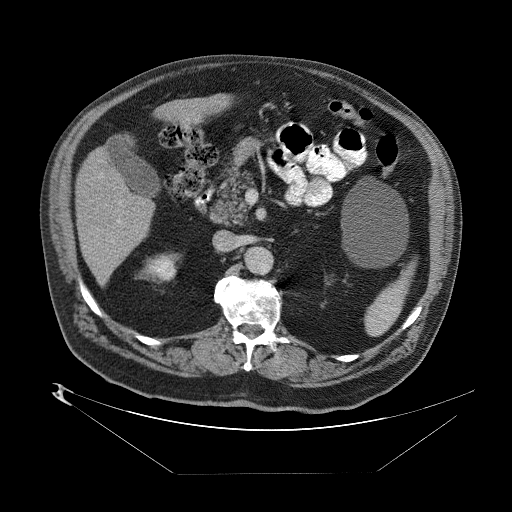
Contrast-enhanced abdominal CT (liver protocol), one axial slice. Slice 30 of 89 in the series (ordered by position). One of 2 acquisitions stored at this slice position. Soft-tissue window (W 400 / L 40 HU). 512 × 512 image matrix, field of view 480 × 480 mm. Case-level facts recorded for this patient, not image findings: diagnosis: hepatocellular carcinoma (patient treated with transarterial chemoembolisation; whether this scan precedes or follows treatment is not stated here); TNM stage (as recorded): Stage-II; Child-Pugh class: B; tumour differentiation: moderately differentiated; tumour size: 4 cm.
Outlined on this slice (semi-automatically segmented with operator editing):
- abdominal aorta: box from (x=247, y=250) to (x=271, y=275) px
- liver parenchyma outside the tumour (the mass and vessels are separate outlines, so this box may not span the whole liver): (x=74, y=140)–(x=154, y=286)
- liver vessels: (x=86, y=217)–(x=122, y=271)